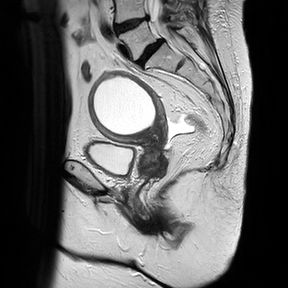
Pelvic MRI for cervical cancer, one sagittal slice; position 14 of 30 along the scan axis; T2-weighted; 1.5 T; TE 100 ms, TR 4816.3 ms; 4 mm slice thickness; 288 × 288 image matrix. Female patient, age 74 years.
Annotated regions visible in this slice (outlined manually by an expert reader):
- uterus and cervix: bounding box (x1, y1, x2, y2) in pixels: (87, 69, 169, 180)